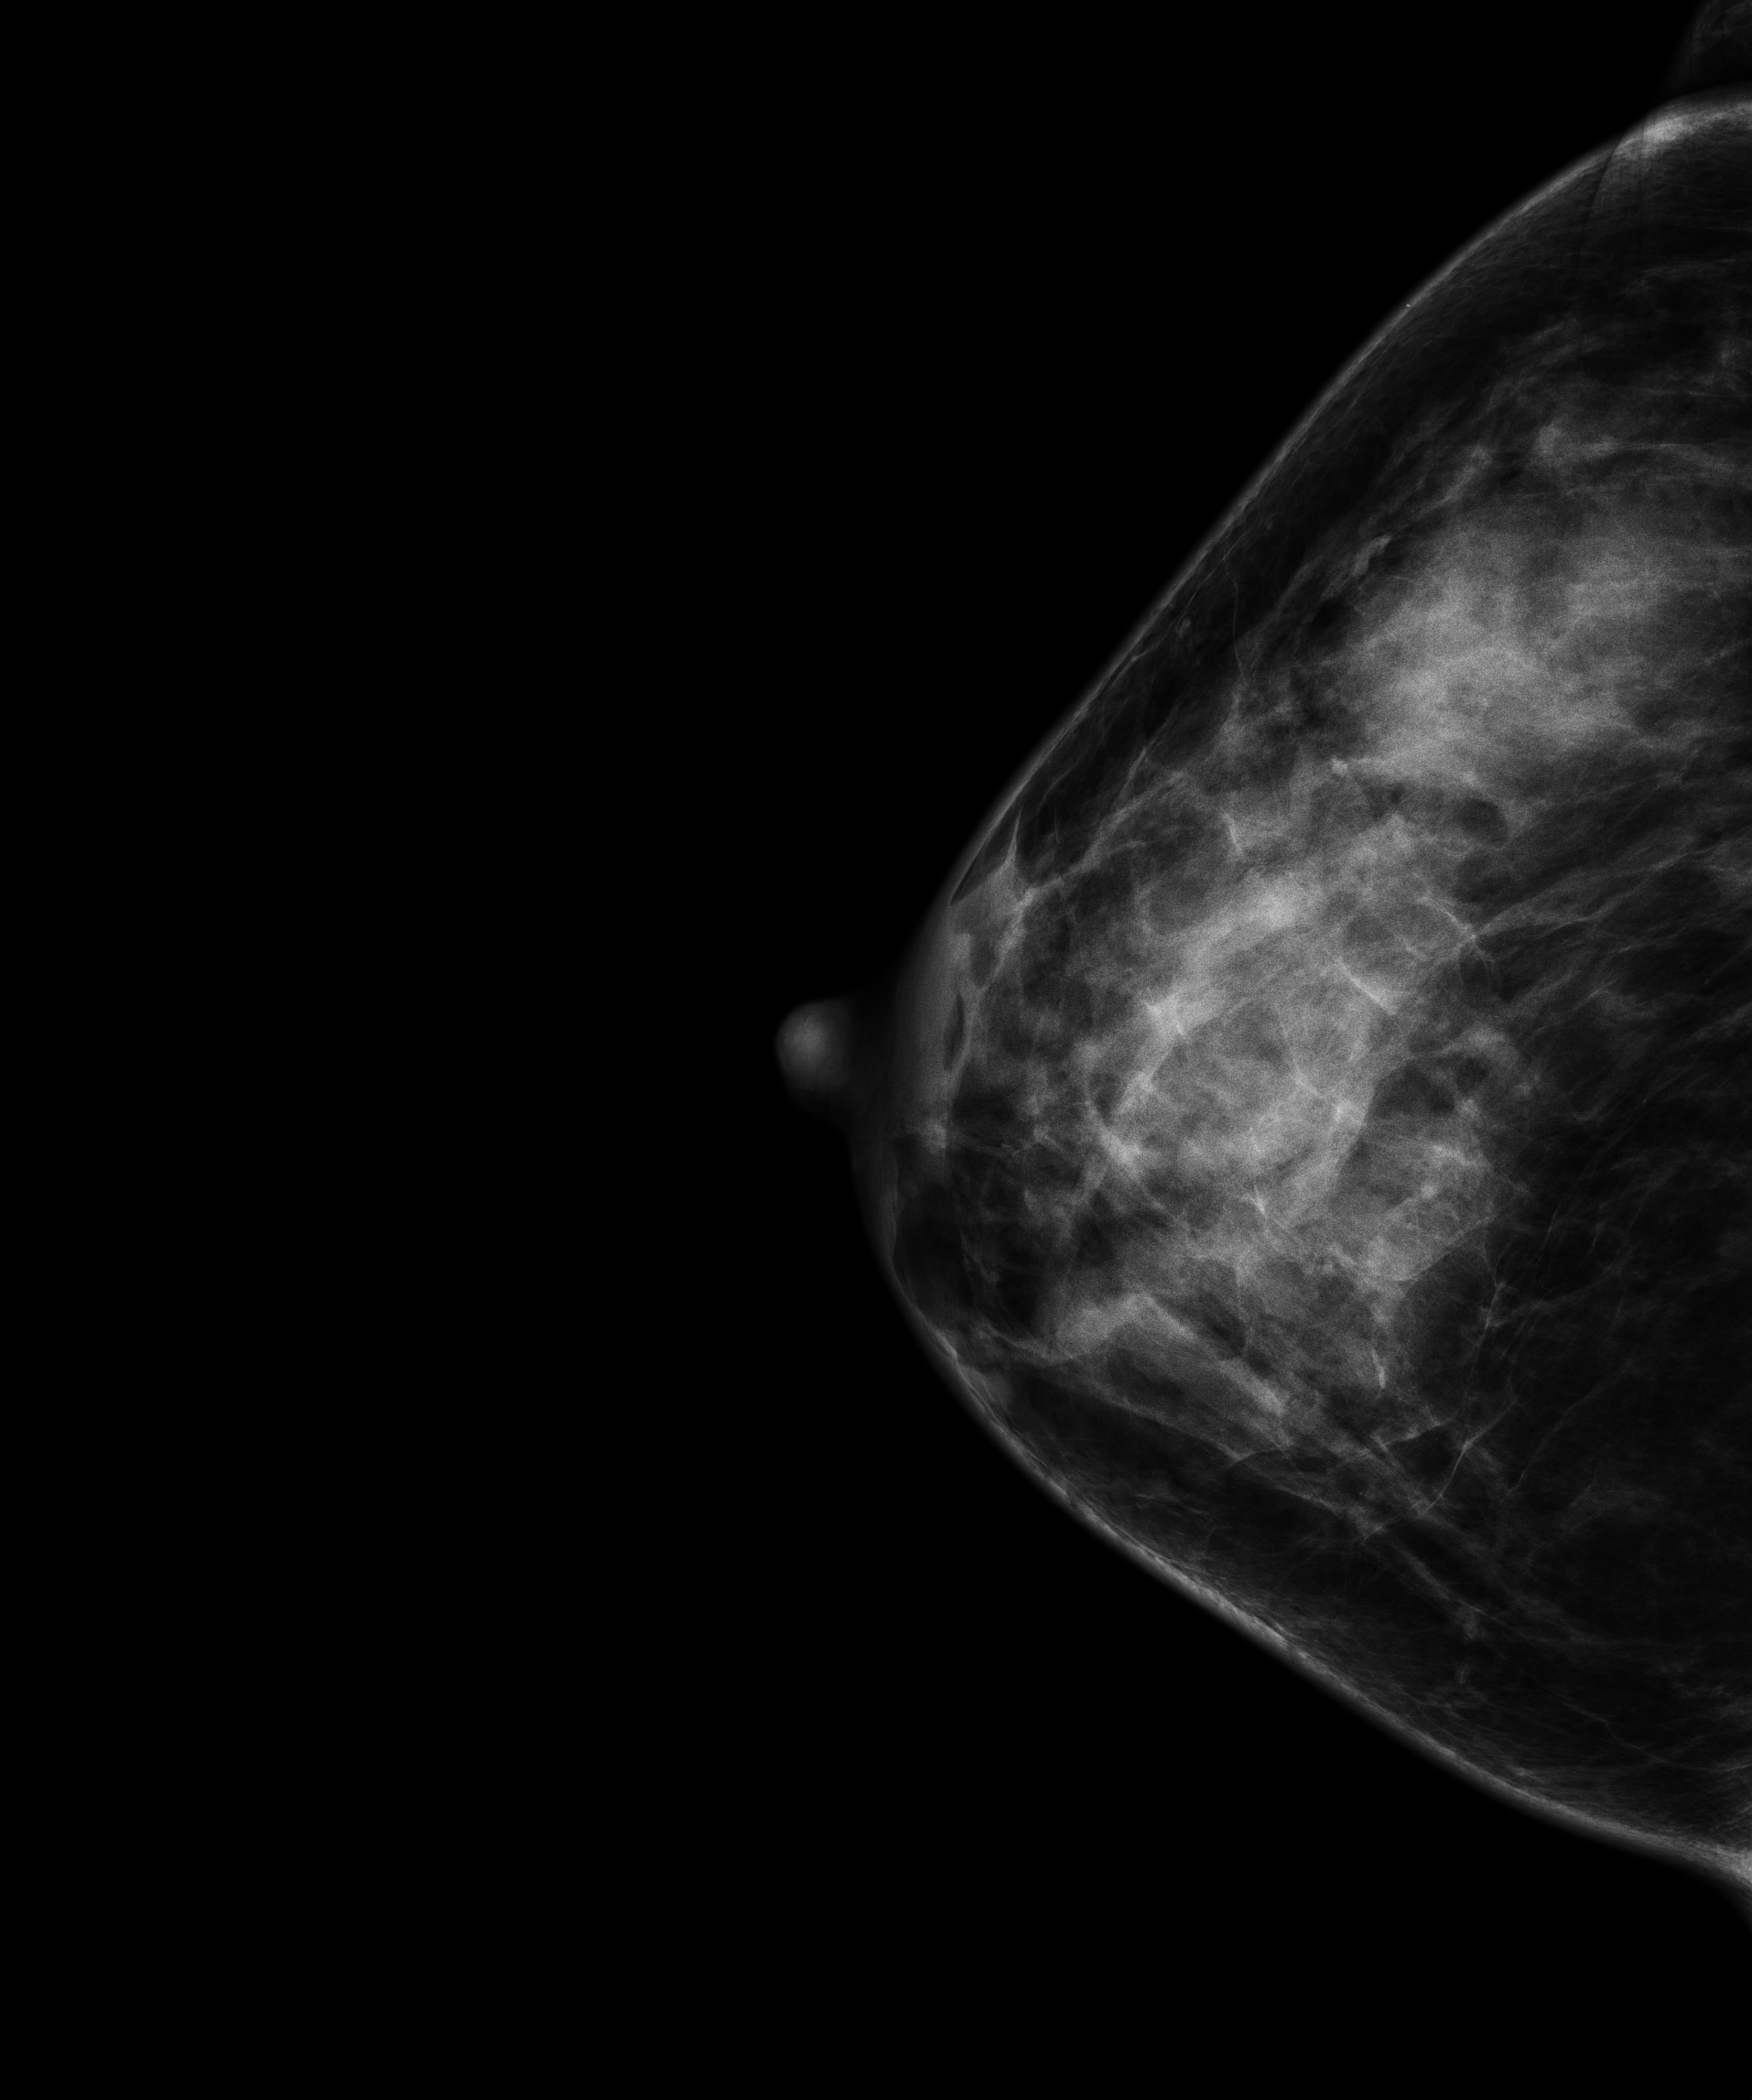
Digital mammogram (FFDM), right breast, cranio-caudal projection, annual screening mammography examination, system: Senographe Essential ADS_56.21.3. Patient aged 55 years (female).
BI-RADS breast density category at the screening exam (both breasts, scale 1–4): 3. Final BI-RADS category for the screening round (tomosynthesis exam, both breasts): category 1. Recall: no recall after this screen.